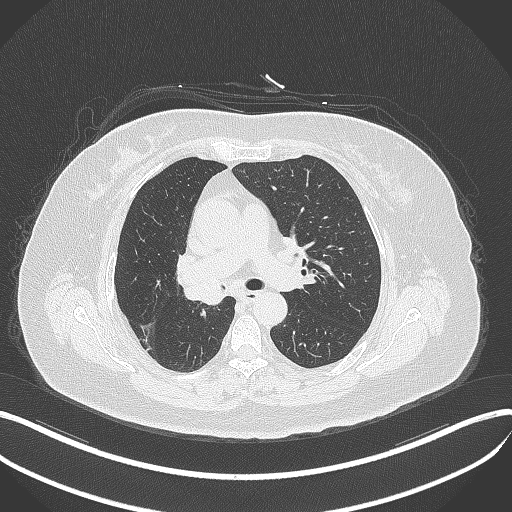
Chest CT, one axial slice. Slice 220 of 376 in the series (ordered by position). 120 kVp. Lung window (W 1500 / L -600 HU). 1 mm slice thickness. 512 × 512 image matrix. Female patient, age 60 years. Case-level facts recorded for this patient, not image findings: clinical TNM (as recorded): T1c N0 M0.
Outlined on this slice (rectangle marked by the reading radiologist):
- lung tumour (recorded histology: squamous cell carcinoma): bounding box [x1, y1, x2, y2] px = [183, 270, 232, 307]